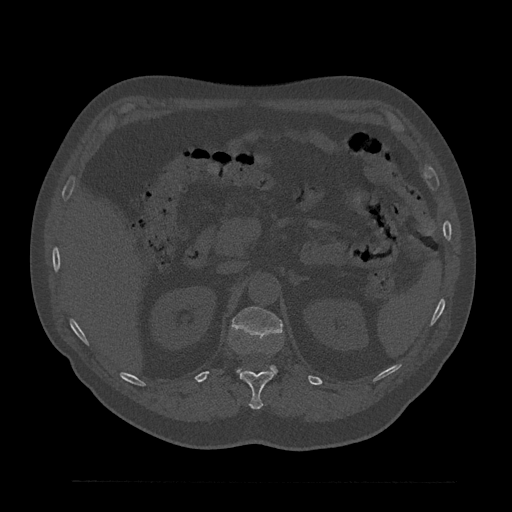
CT including the spine, one axial slice. Slice 204 of 797 in the series (ordered by position). Bone window (W 1800 / L 400 HU). 0.5 mm slice thickness. 512 × 512 image matrix, field of view 430 × 430 mm. Patient: male, 61 years. Case-level facts recorded for this patient, not image findings: primary cancer: prostate.
Annotated regions visible in this slice (semi-automatically segmented with operator editing):
- L1 vertebra: bounding box (x1, y1, x2, y2) in pixels: (232, 307, 282, 374)
- T12 vertebra: (239, 371, 273, 410)